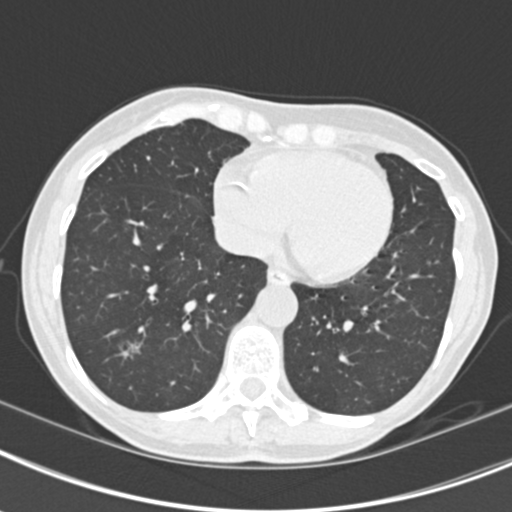
Chest CT (low-dose screening protocol), one axial image; second screening round (one year after baseline); lung window (W 1500 / L -600 HU); standard (soft-tissue) reconstruction kernel (B30f); slice 135 of 219 in the series; 512 × 512 image matrix, field of view 298 × 298 mm. Female, age 63 years at enrolment. Current smoker at enrolment.
• Lesion marked by an expert reader, bounding box <110,327,153,369> (left, top, right, bottom; pixels).
• The screening reader recorded 9 non-calcified nodules or masses ≥4 mm on this exam (left upper lobe, right upper lobe, left upper lobe, left lower lobe, right middle lobe, left lower lobe, left lower lobe, right lower lobe, right lower lobe); which of them this box marks is not recorded.
• Later outcome: lung cancer diagnosed 408 days after this screen — bronchiolo-alveolar adenocarcinoma, NOS, right upper lobe, right middle lobe, right lower lobe, left upper lobe, left lower lobe, moderately differentiated (G2), stage IV (AJCC 6th edition).